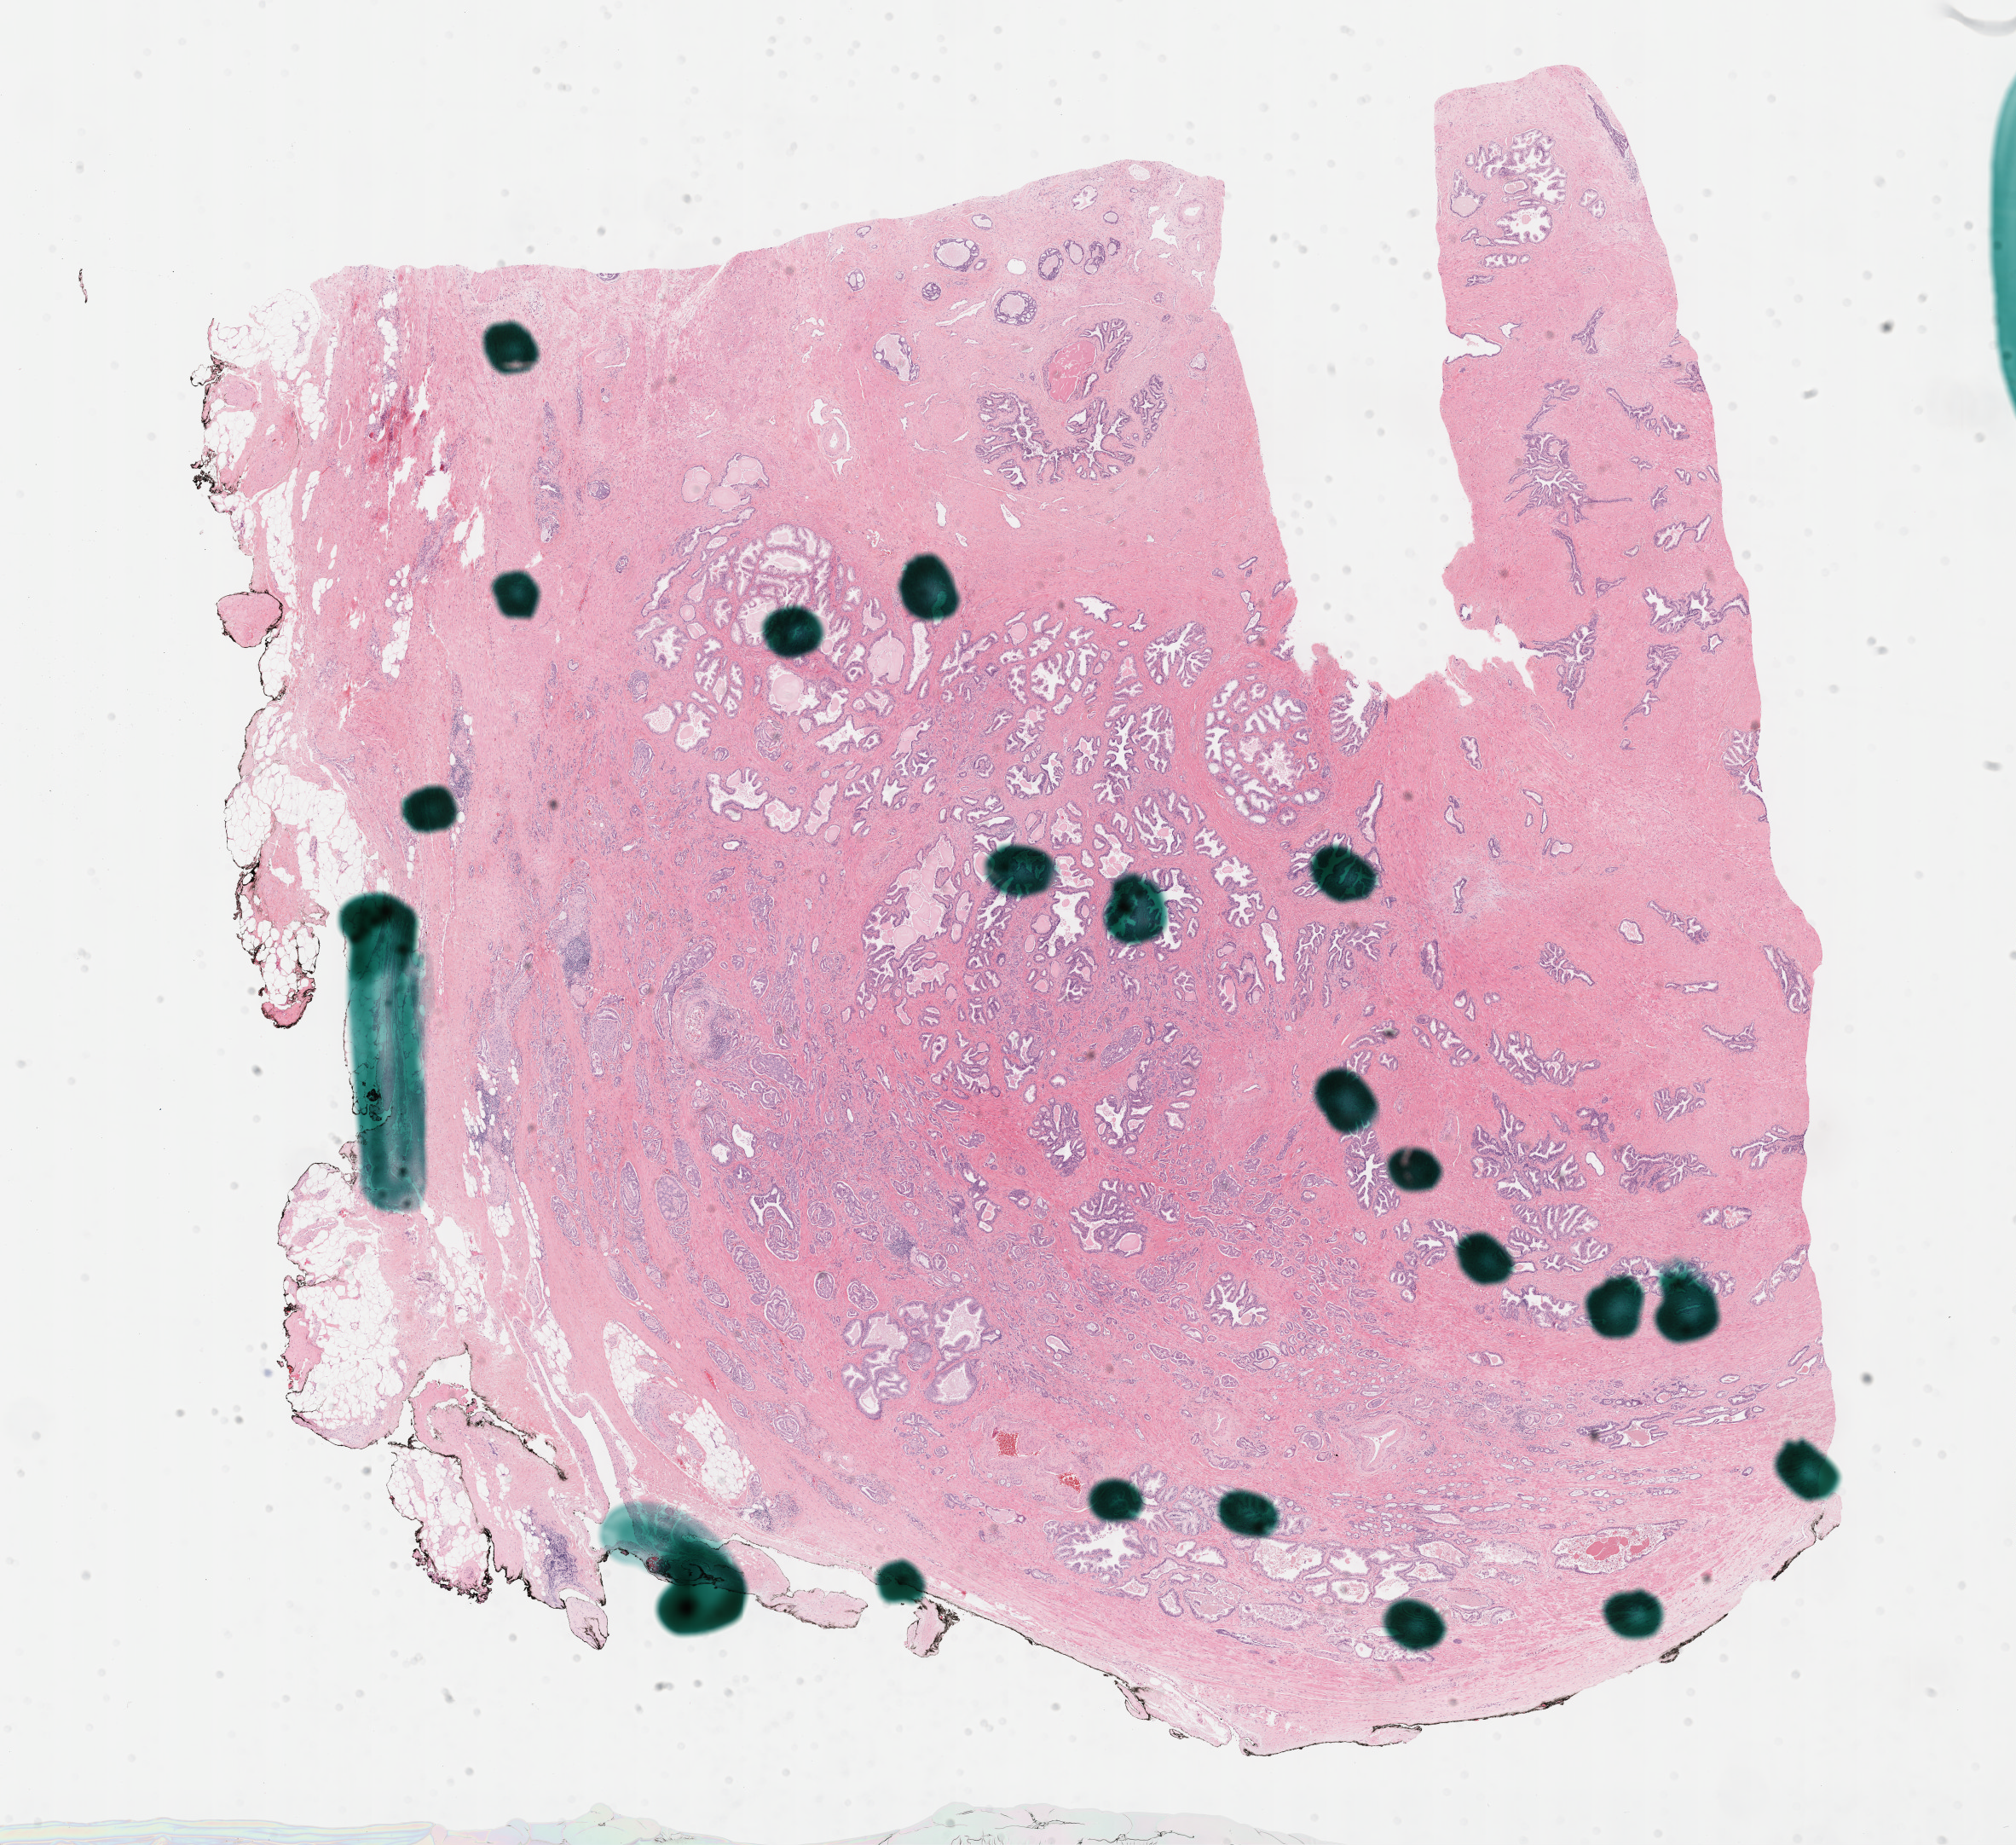
Digitized H&E-stained tissue section (whole slide) — low-resolution overview of the scanned area, about 19.1 x 17.5 mm (acquisition: 40x scan). Formalin-fixed paraffin-embedded (FFPE) diagnostic section. Primary tumour sample from the prostate. Patient: male, age at initial diagnosis 58 years. Gleason score: 7 (3+4).
* laterality: bilateral
* diagnosis: Adenocarcinoma, NOS (prostate gland)
* lymph nodes positive (case pathology): 1 of 16 examined